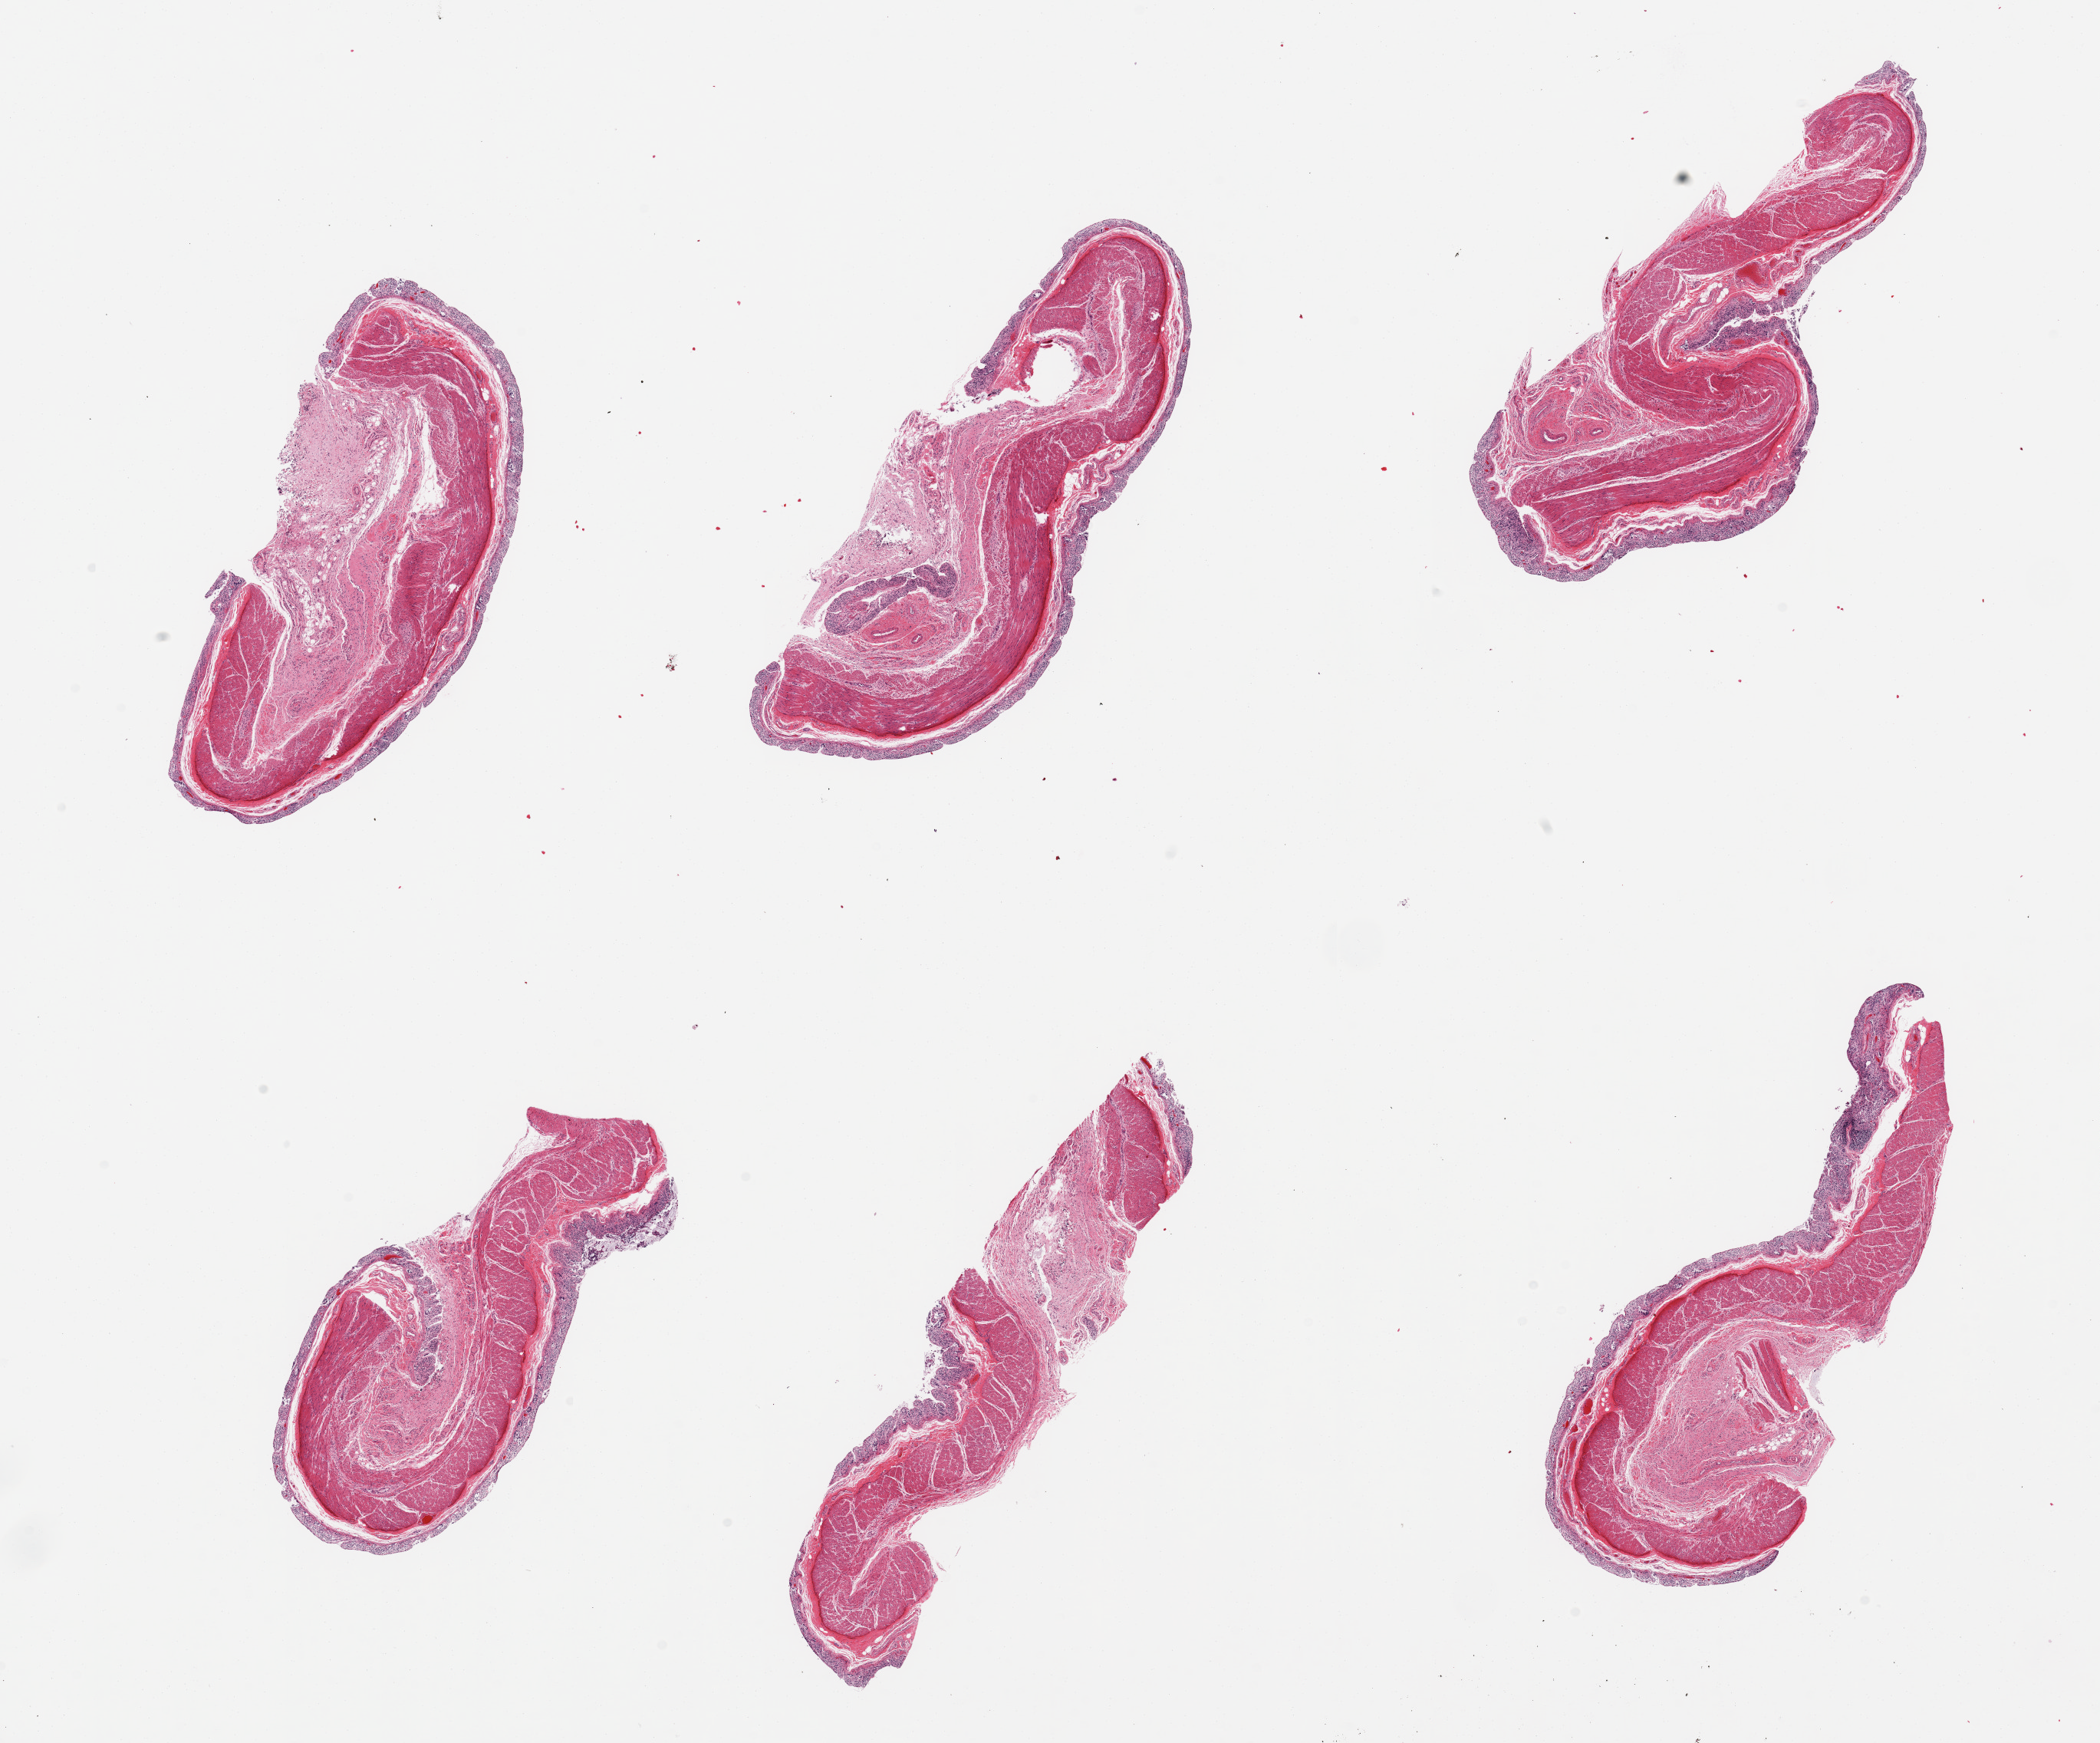
Whole-slide image, hematoxylin and eosin (H&E) stain, low-resolution overview of the scanned area, about 21.7 x 18.0 mm, PAXgene-fixed, paraffin-embedded tissue, section of transverse colon (target tissue), tissue donor sample.
Pathologist's review note for this sample: 6 pieces, glandular portions of mucosa totally autolyzed.